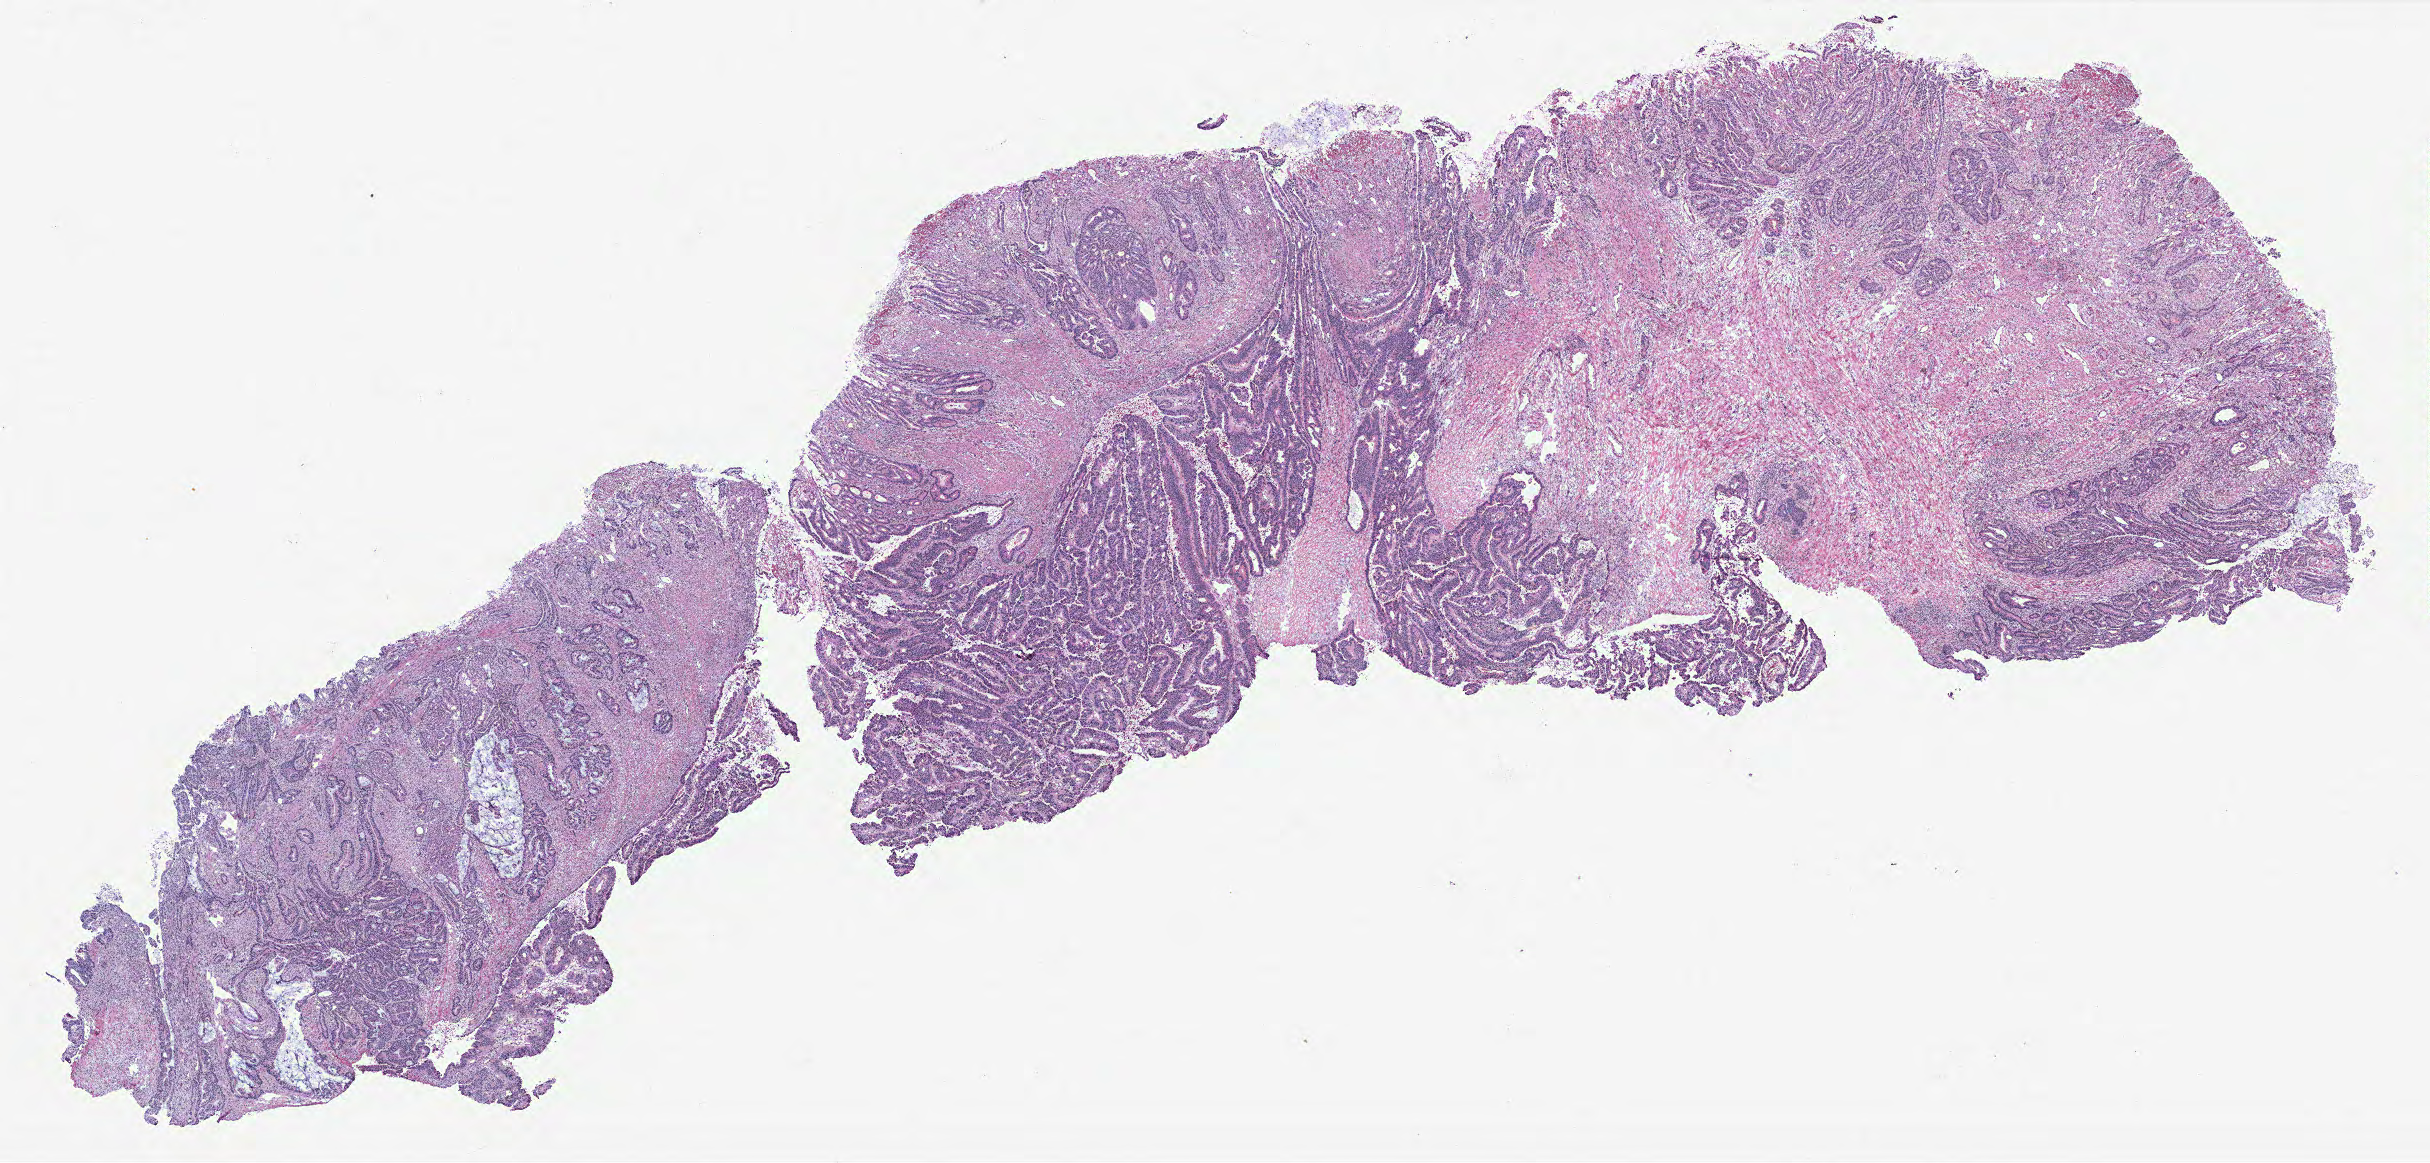
Digitized Hematoxylin and eosin (H&E) stained tissue section (whole slide), low-resolution overview of the scanned area, about 19.4 x 9.3 mm; normal (non-tumour) tissue sample, colon. 87-year-old male patient.
This section: normal (non-tumour) tissue from the same patient. Patient diagnosis: Adenocarcinoma, NOS.